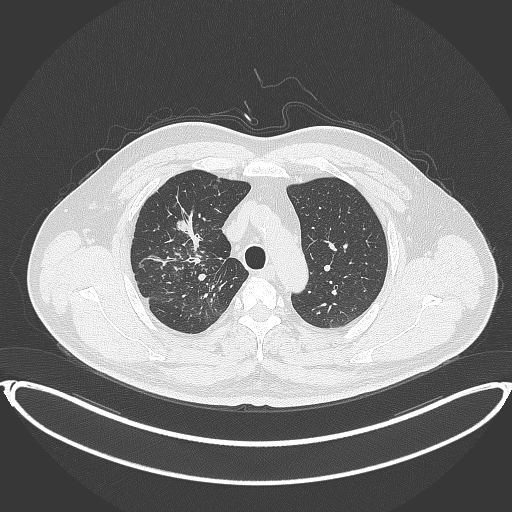
Chest CT, one axial slice. Position 296 of 399 along the scan axis. Reconstruction kernel B70f. 120 kVp. Lung window (W 1500 / L -600 HU). 1 mm slice thickness. 512 × 512 image matrix, field of view 445 × 445 mm. Male patient, age 53 years. Case-level facts recorded for this patient, not image findings: clinical TNM (as recorded): T2a N0 M0.
Structures marked on this image (rectangle marked by the reading radiologist):
- lung tumour (recorded histology: adenocarcinoma): bounding box (x1, y1, x2, y2) in pixels: (173, 214, 192, 235)